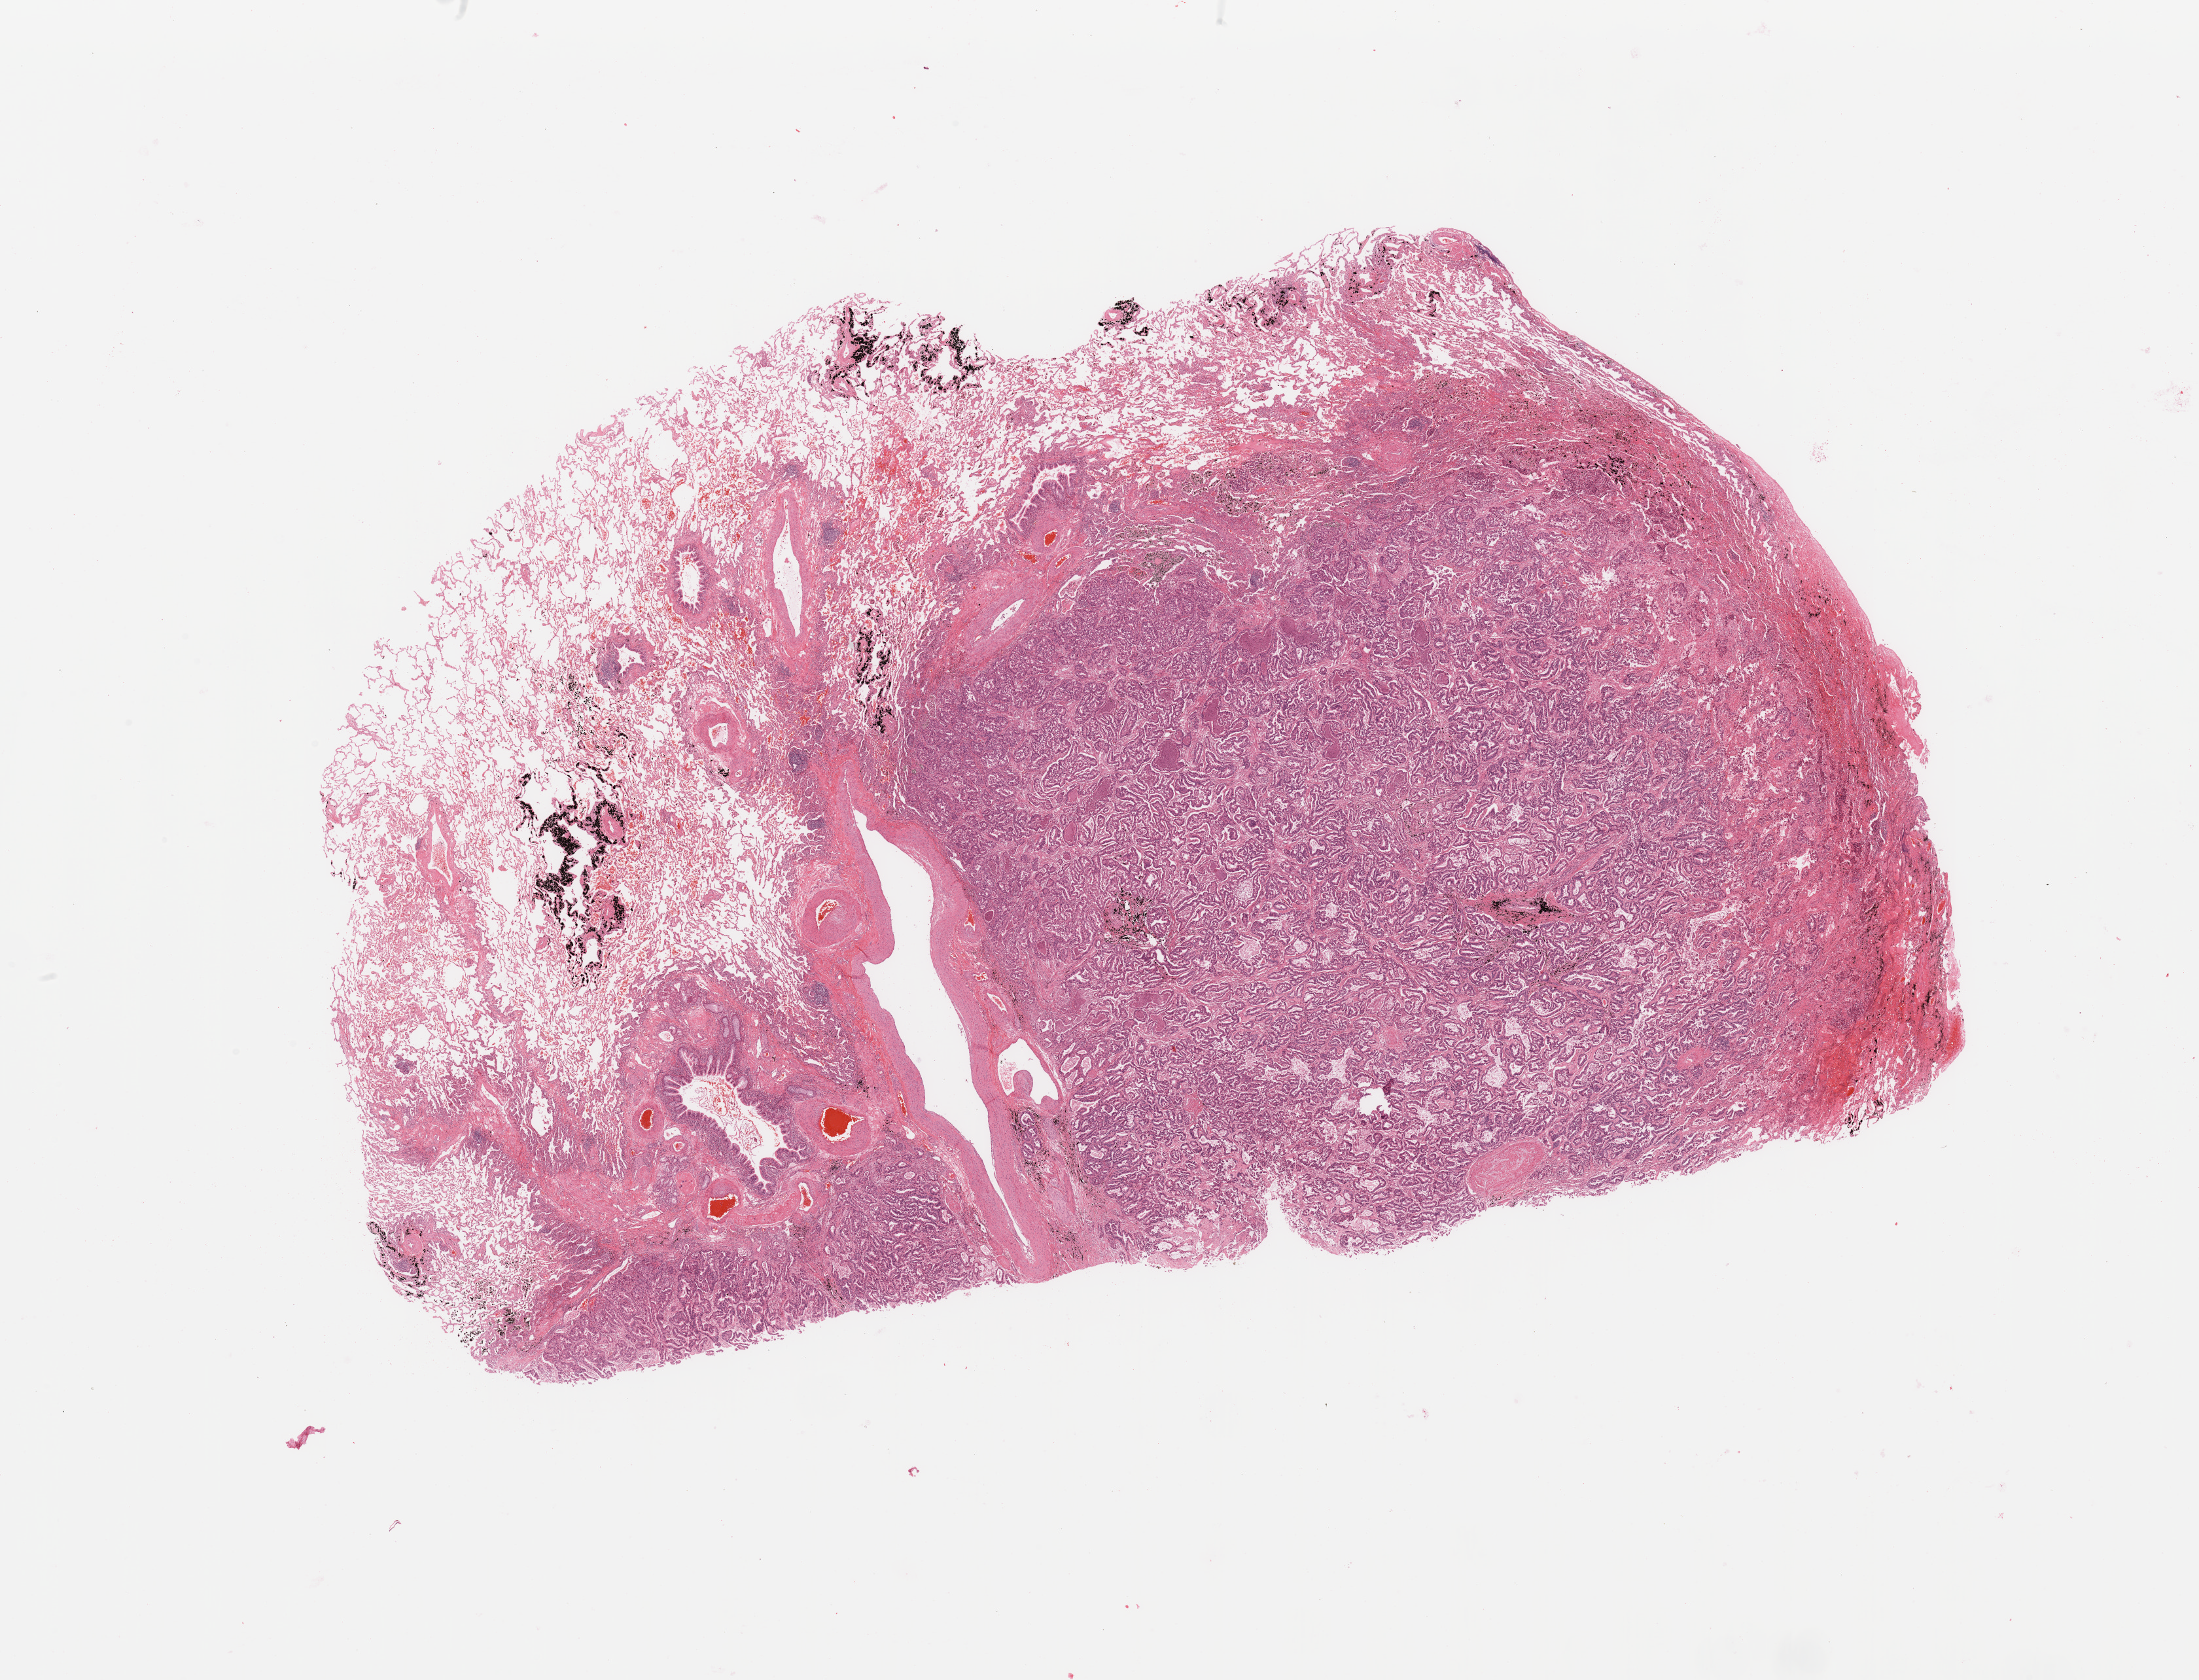
Whole-slide histology image, H&E — low-resolution overview of the scanned area, about 26.6 x 20.3 mm (acquisition: 20x scan), tumour tissue sample, lung. Male, 59 y/o. Histologic grade: G2 (moderately differentiated).
Primary tumour site (as recorded): left upper lobe. AJCC pathologic stage: IB. Diagnosis: Adenocarcinoma, NOS.